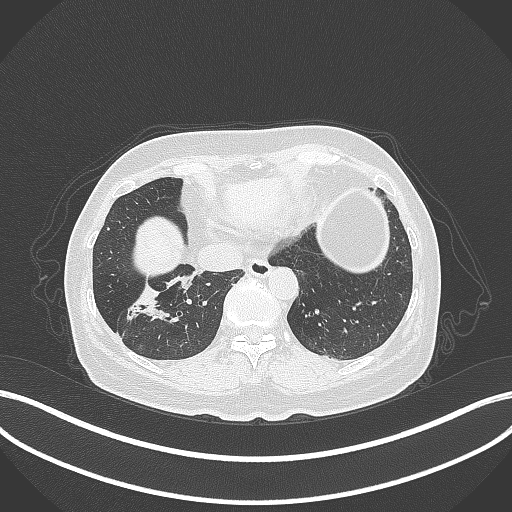
Chest CT, one axial slice; lung window (W 1500 / L -600 HU); 1 mm slice thickness; 512 × 512 image matrix, field of view 400 × 400 mm. Female patient, age 67 years. From the clinical record (not read from this slice): clinical TNM (as recorded): T1c N1 M0; histopathological grade: G2-3.
Annotated regions visible in this slice (bounding box drawn by a radiologist):
- lung tumour (recorded histology: adenocarcinoma): bounding box (x1, y1, x2, y2) in pixels: (125, 275, 192, 330)